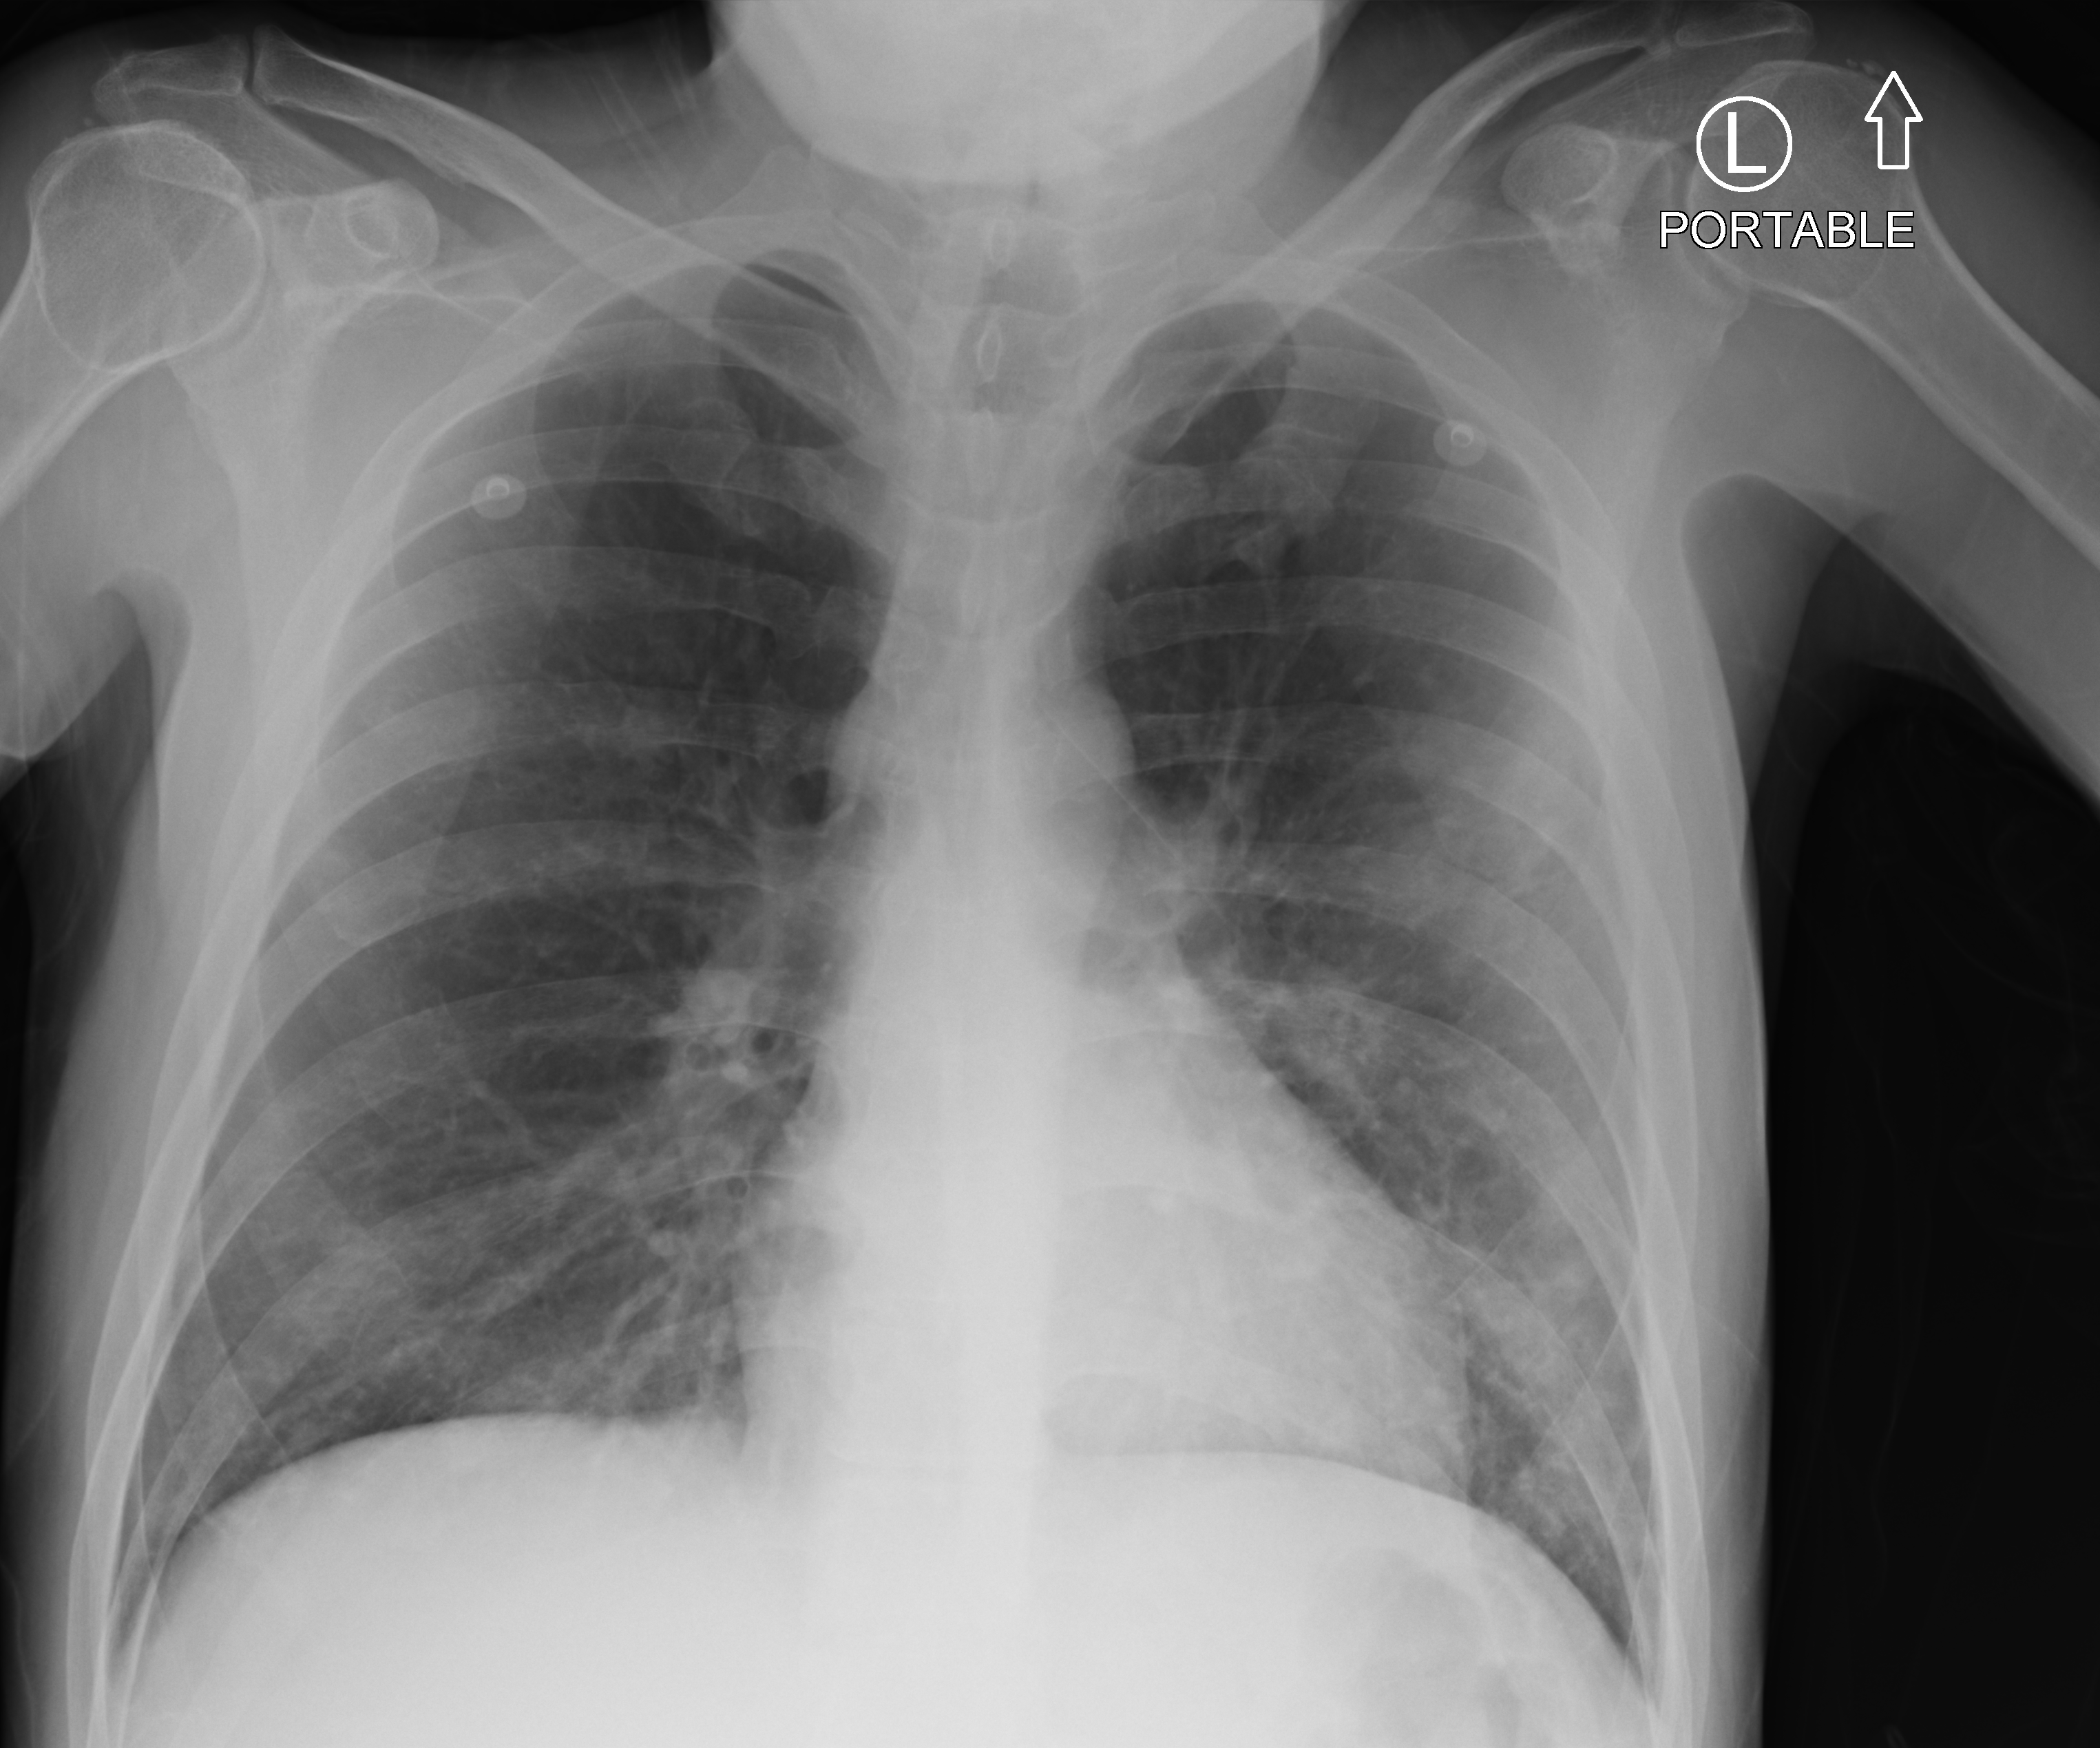
Bedside chest radiograph (computed radiography), anteroposterior (AP) projection. Patient hospitalised with COVID-19; male, aged 18–59 years.
Hospital-stay facts (about this admission, not read from this image; timing relative to this image not recorded): admitted to intensive care during this hospital stay: no; length of hospital stay: 1 day.